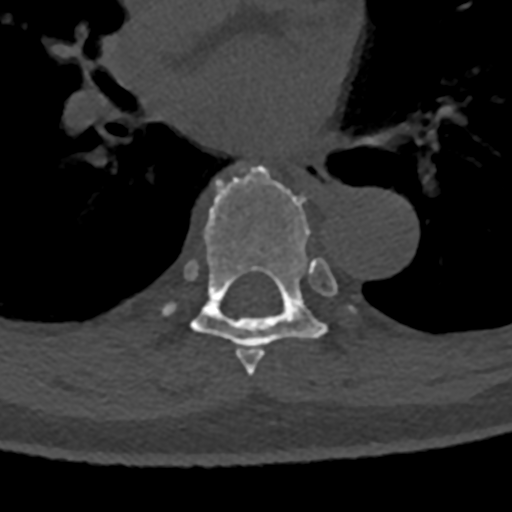
CT including the spine, one axial slice. Position 766 of 797 along the scan axis. Reconstruction kernel Br40s/3. Bone window (W 1800 / L 400 HU). 0.5 mm slice thickness. 512 × 512 image matrix. Patient: male, 74 years. Case-level facts recorded for this patient, not image findings: primary cancer: renal; vertebrae with lytic lesions (as recorded): T10, L1, L2, L3, L4, L5.
Structures marked on this image (semi-automatic segmentation, software-assisted and operator-edited):
- T6 vertebra: bounding box [x1, y1, x2, y2] px = [246, 350, 264, 376]
- T7 vertebra: [157, 165, 348, 367]